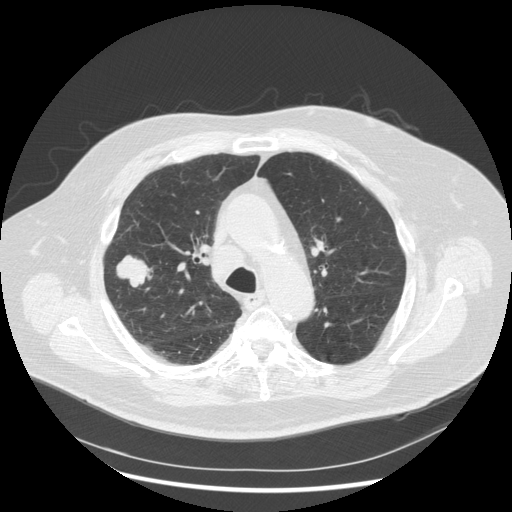
Low-dose screening chest CT, one axial slice; reconstruction kernel STANDARD; lung window (W 1500 / L -600 HU); 2.5 mm slice thickness; 512 × 512 image matrix, field of view 400 × 400 mm.
Structures marked on this image (outlined manually by an expert reader):
- lesion 1 (tumor, upper lobe of right lung): bounding box (x1, y1, x2, y2) in pixels: (117, 255, 151, 289)